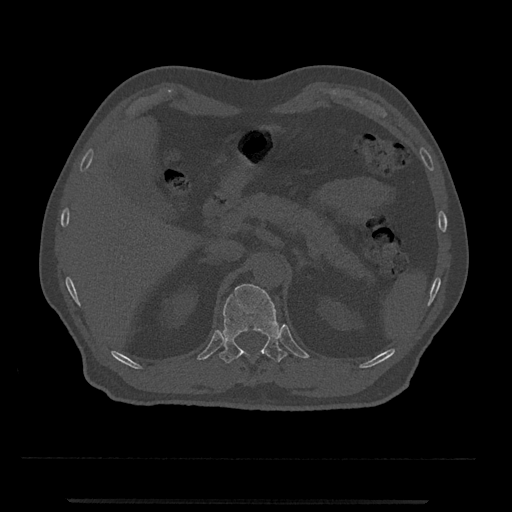
CT including the spine, one axial slice. Slice 411 of 797 in the series (ordered by position). 120 kVp. Bone window (W 1800 / L 400 HU). 512 × 512 image matrix, field of view 419 × 419 mm. Male patient, age 63 years. Case-level facts recorded for this patient, not image findings: primary cancer: prostate.
Annotated regions visible in this slice (semi-automatically segmented with operator editing):
- T12 vertebra: box from (x=219, y=284) to (x=288, y=363) px